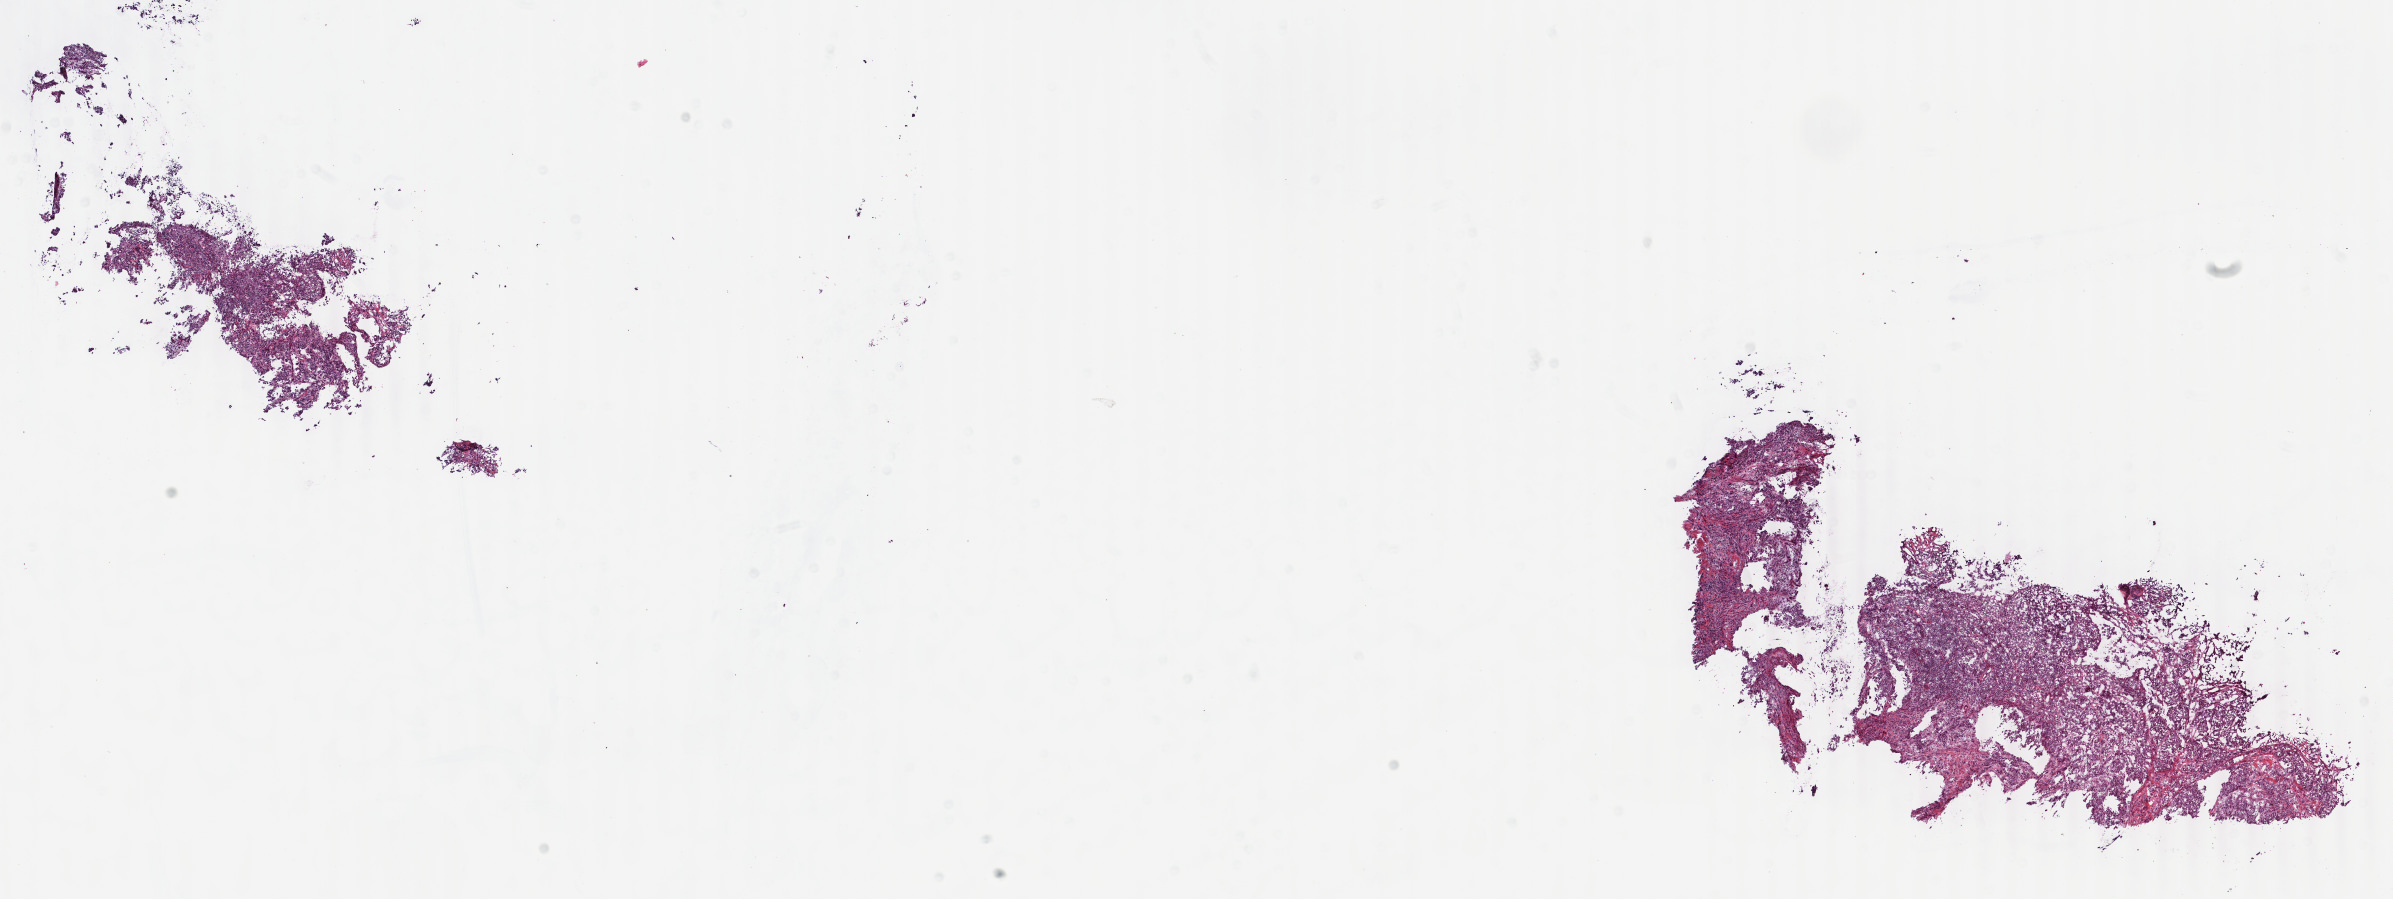
Digitized Hematoxylin and eosin (H&E) stained tissue section (whole slide), low-resolution overview of the scanned area, about 19.0 x 7.2 mm; frozen section; primary tumour sample from the breast. Patient: female, age at initial diagnosis 34 years. Composition of this section per pathologist review: tumour cells 85%, tumour nuclei 85%, normal cells 0%, stromal cells 12%, necrosis 3%. Infiltration values recorded for this section: lymphocyte infiltration 2%, monocyte infiltration 1%, neutrophil infiltration 0%.
• diagnosis: Infiltrating duct carcinoma, NOS
• AJCC pathologic stage: IIA